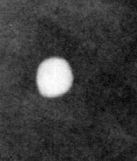
Region of interest cut from a scanned film mammogram (one marked finding), left breast, MLO view.
Marked abnormality: calcifications, morphology round and regular / lucent center / punctate, distribution diffusely scattered; BI-RADS assessment category 2; subtlety rating 5 on a 1 (subtle) to 5 (obvious) scale; benign; no additional work-up was recommended (benign without callback).